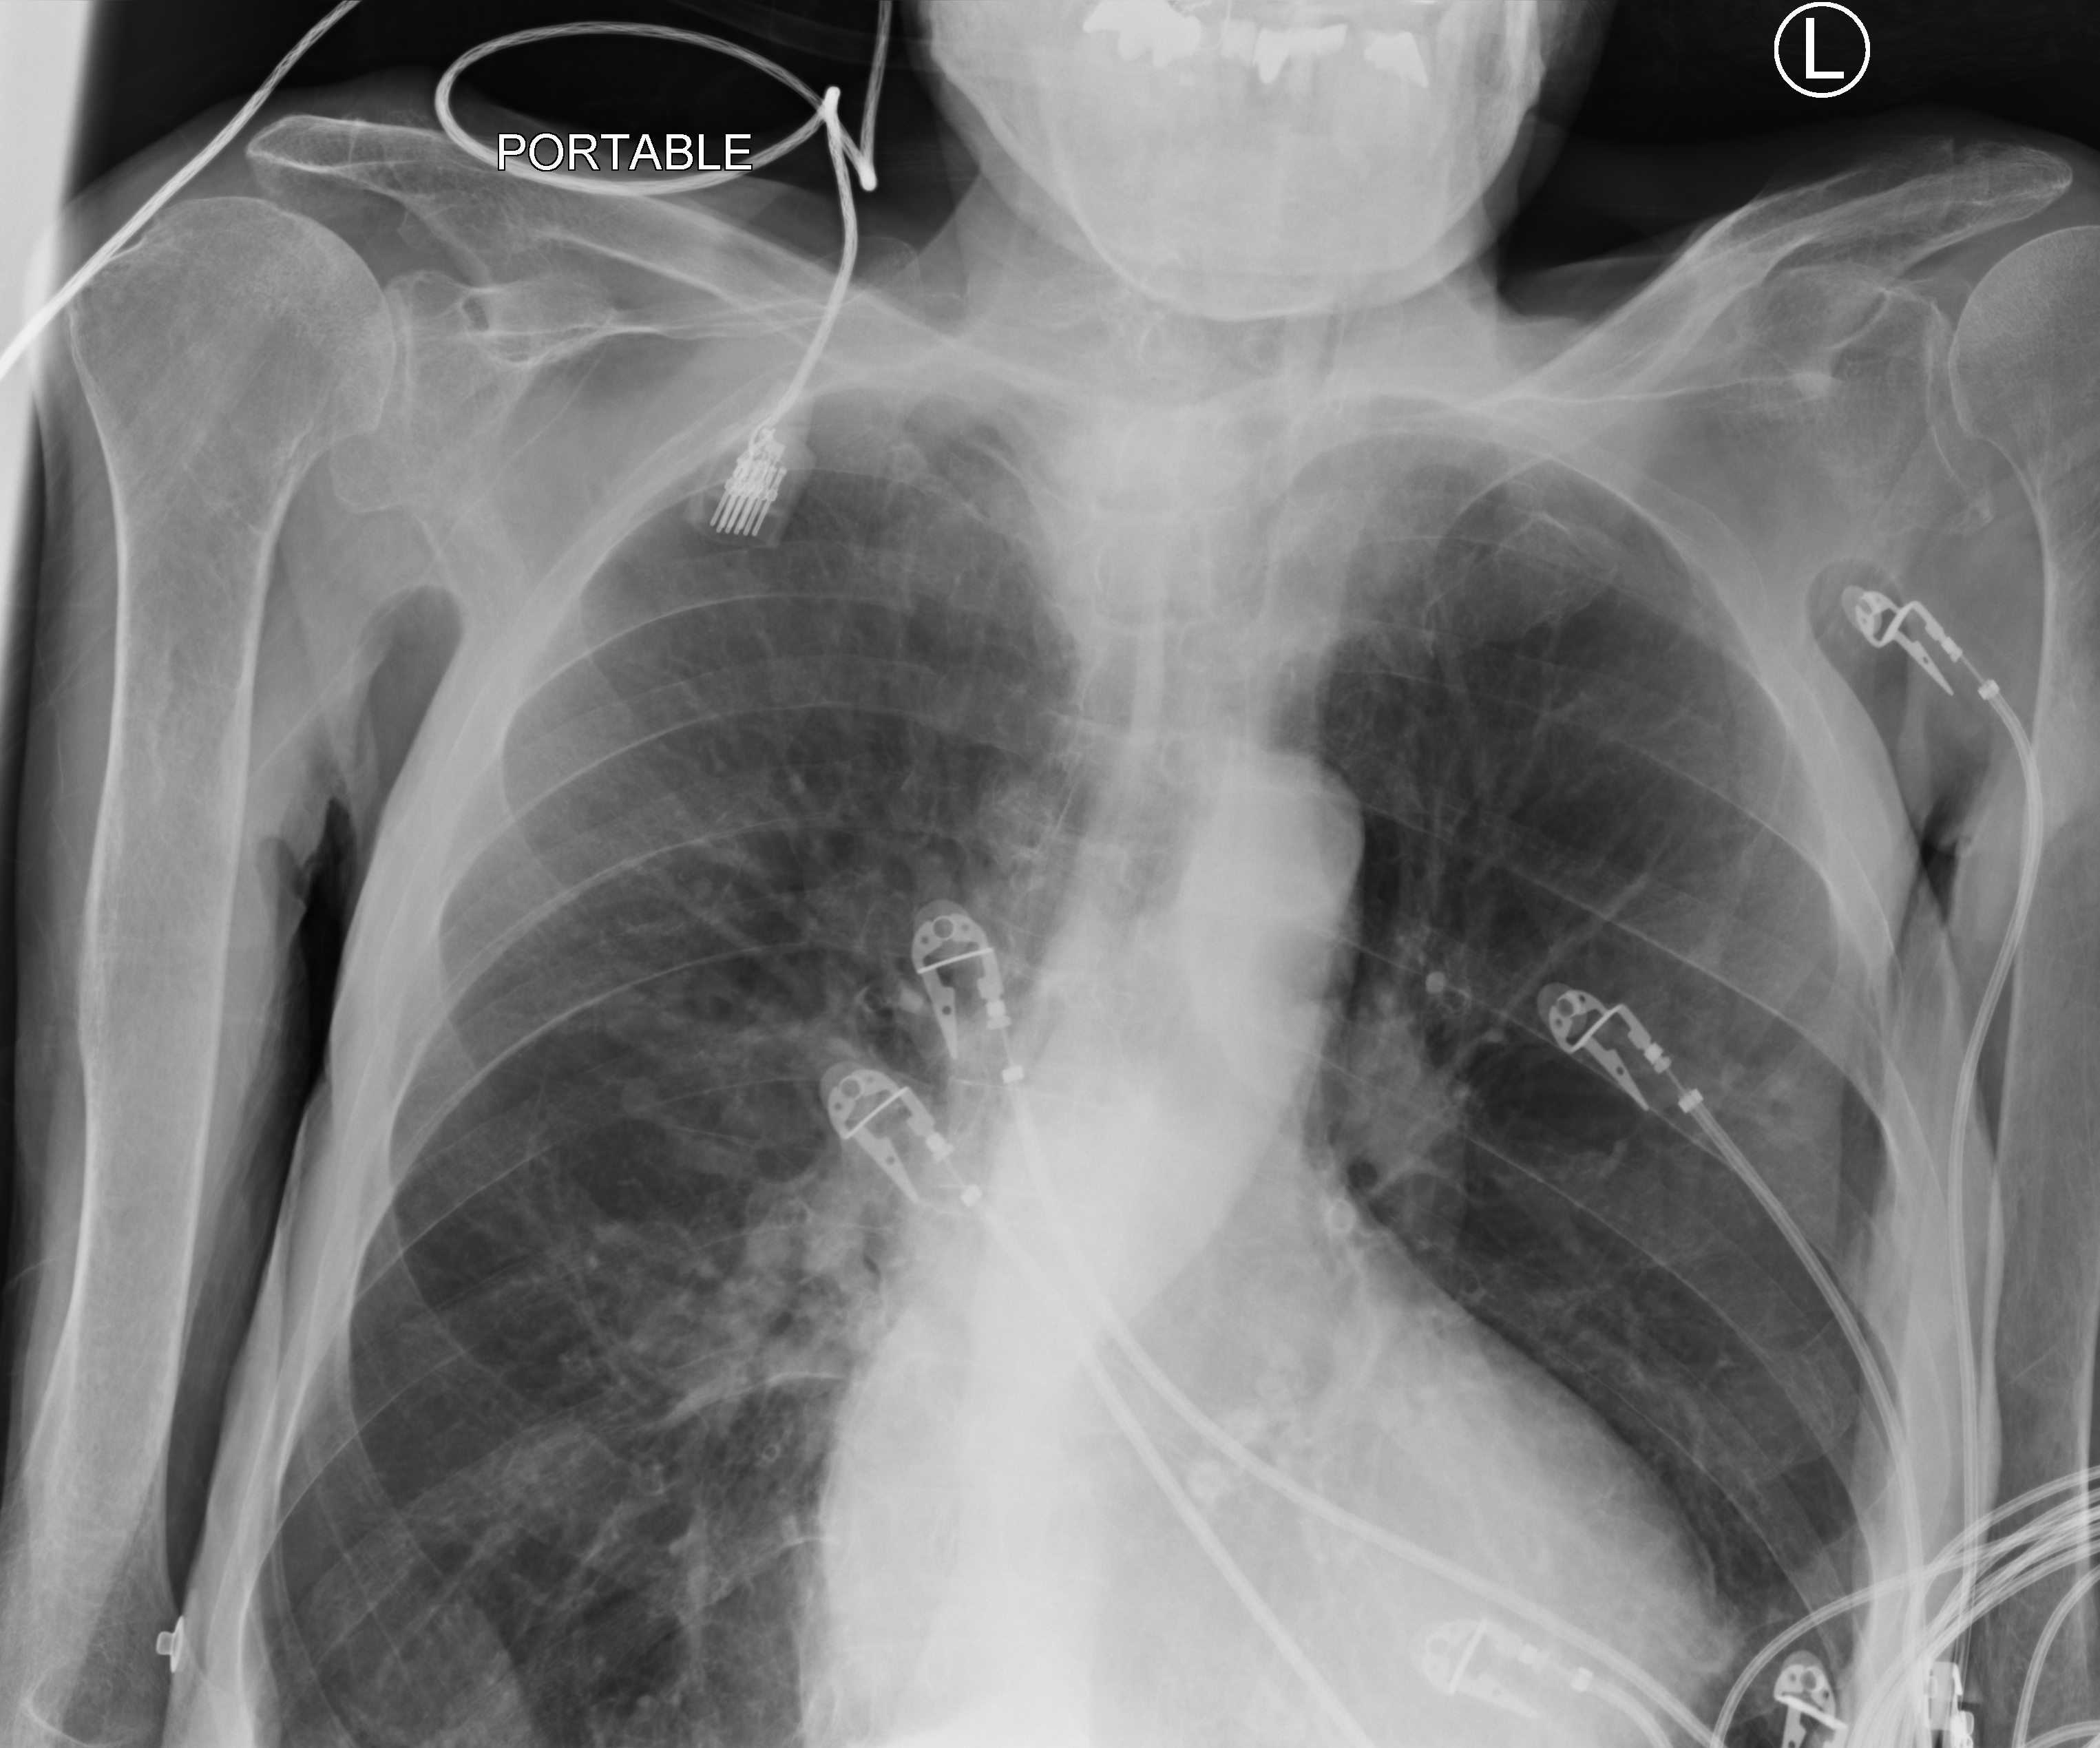
Bedside chest radiograph (computed radiography); anteroposterior (AP) projection. Male patient hospitalised with COVID-19, age 75–90 years.
From the hospital-stay record, not from the radiograph (when in the stay this image was taken is not recorded): admitted to intensive care during this hospital stay: no; mechanically ventilated during this hospital stay: no.